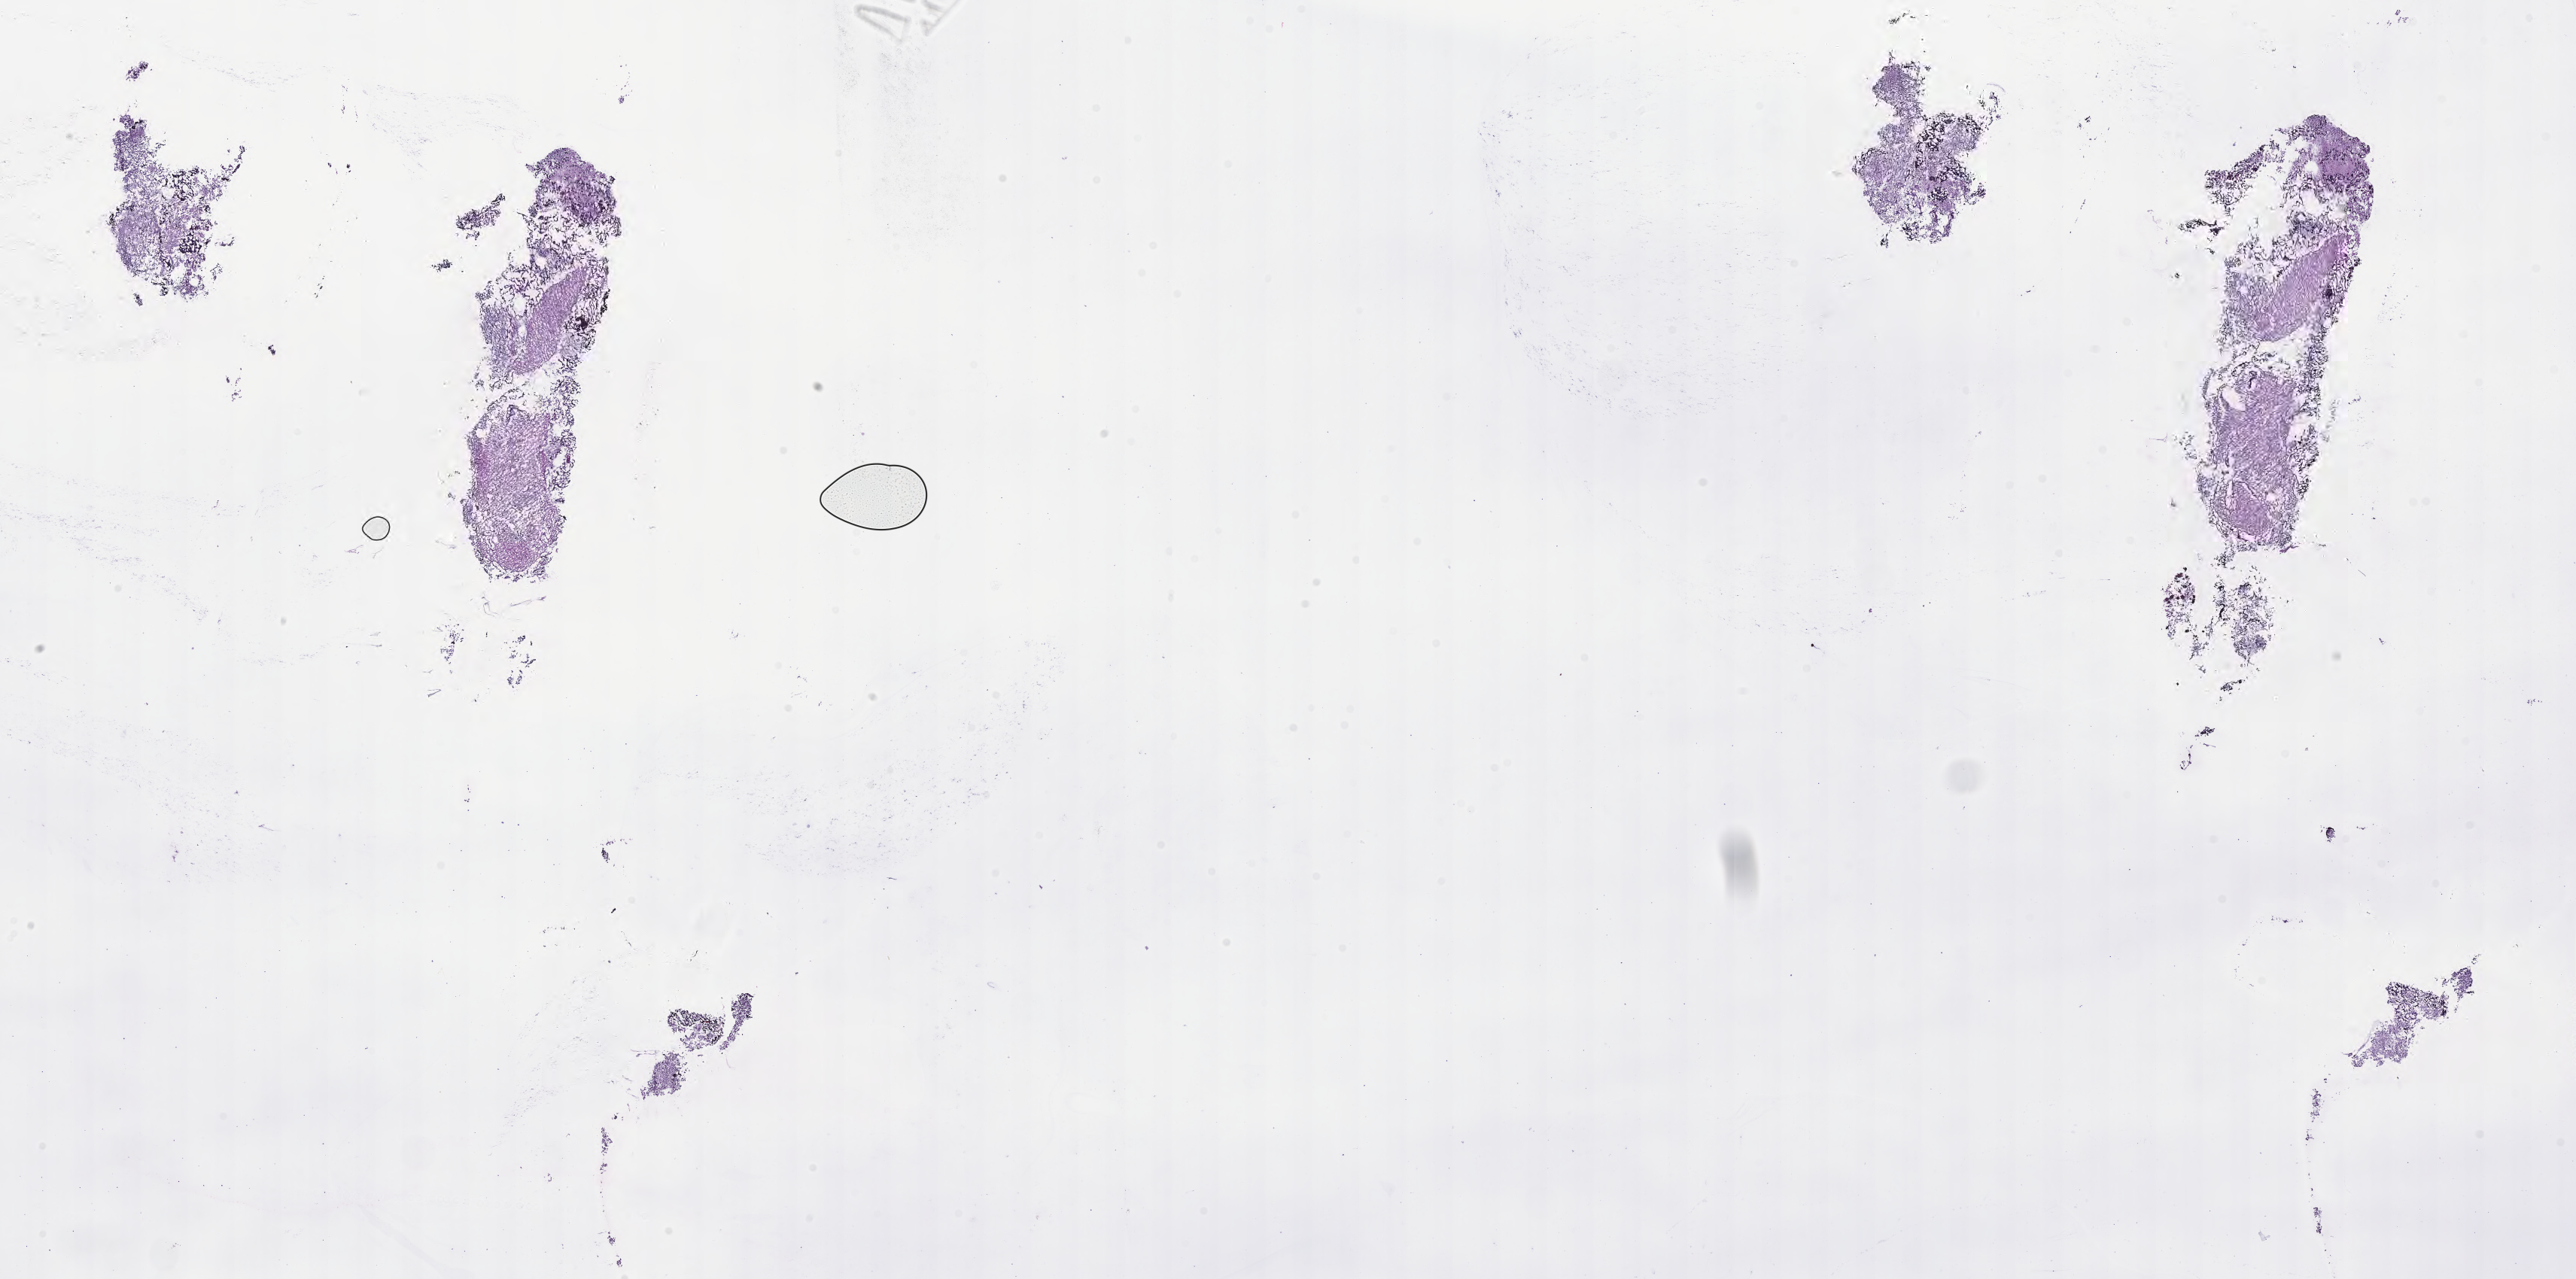
Whole-slide image, hematoxylin and eosin (H&E) stain of tumor tissue from the brain, shown as a low-resolution overview of the whole scanned area (about 27.7 x 13.7 mm). Frozen section (OCT-embedded). Patient: female, age 76 months.
Recorded diagnosis: Malignant tumor, small cell type.